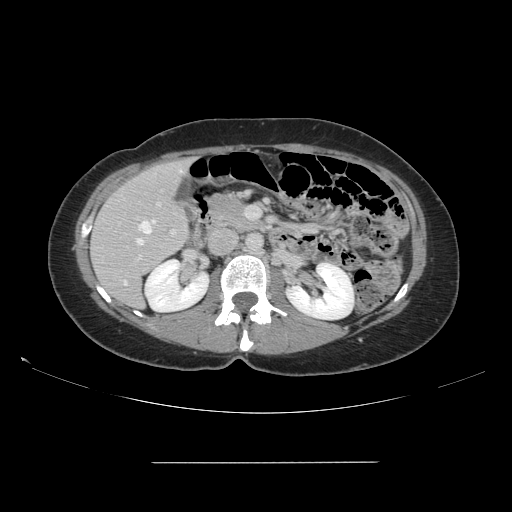
Contrast-enhanced abdominal CT, one axial slice; slice 74 of 151 in the series (ordered by position); intravenous contrast given; soft-tissue window (W 400 / L 40 HU); 2.5 mm slice thickness; 512 × 512 image matrix, field of view 421 × 421 mm. Female patient, age 46 years. Case-level facts recorded for this patient, not image findings: diagnosis: colorectal cancer liver metastases, imaged before liver resection; multiple liver metastases: yes; largest metastasis: 3 cm; disease in both lobes: yes.
Annotated regions visible in this slice (outlined manually by an expert reader):
- hepatic veins: bounding box [x1, y1, x2, y2] px = [136, 220, 155, 245]
- liver: [92, 161, 190, 308]
- planned liver remnant (the part of the liver to remain after resection): [93, 161, 189, 308]
- portal vein (with intrahepatic branches): [136, 202, 177, 261]